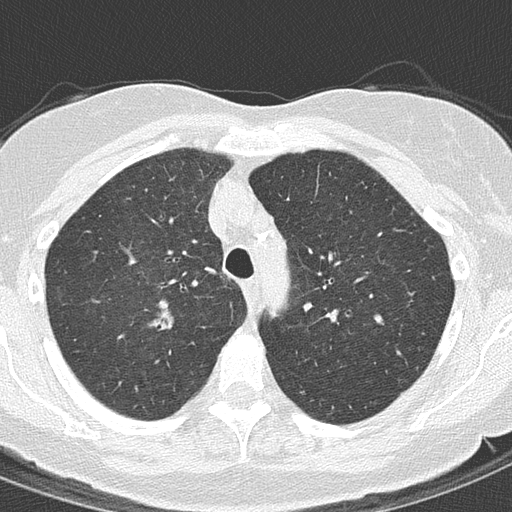
Low-dose screening chest CT, axial slice. Second screening round (one year after baseline). Lung window (W 1500 / L -600 HU). 2 mm slice thickness. Lung (sharp) reconstruction kernel (B50f). 120 kVp. Slice 43 of 157 in the series. Female, age 61 years at enrolment. Current smoker at enrolment.
- Lesion marked by an expert reader, bounding box <147,303,188,340> (left, top, right, bottom; pixels).
- Reader record for this screening exam (exam-level; its link to the box is not recorded): non-calcified nodule or mass ≥4 mm, right upper lobe, 15 × 10 mm, spiculated (stellate) margins, ground glass attenuation, pre-existing on the prior screen: yes; interval growth: yes.